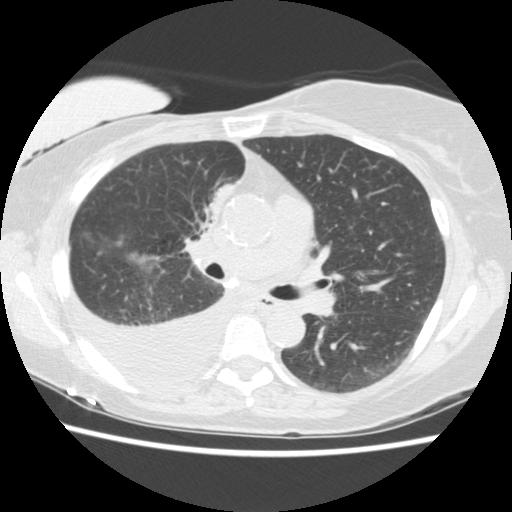
Low-dose screening chest CT, one axial slice. Slice 88 of 157 in the series (ordered by position). Lung window (W 1500 / L -600 HU). 2.5 mm slice thickness. 512 × 512 image matrix.
Annotated regions visible in this slice (expert manual segmentation):
- lesion 1 (tumor, upper lobe of right lung): box from (x=208, y=183) to (x=233, y=216) px